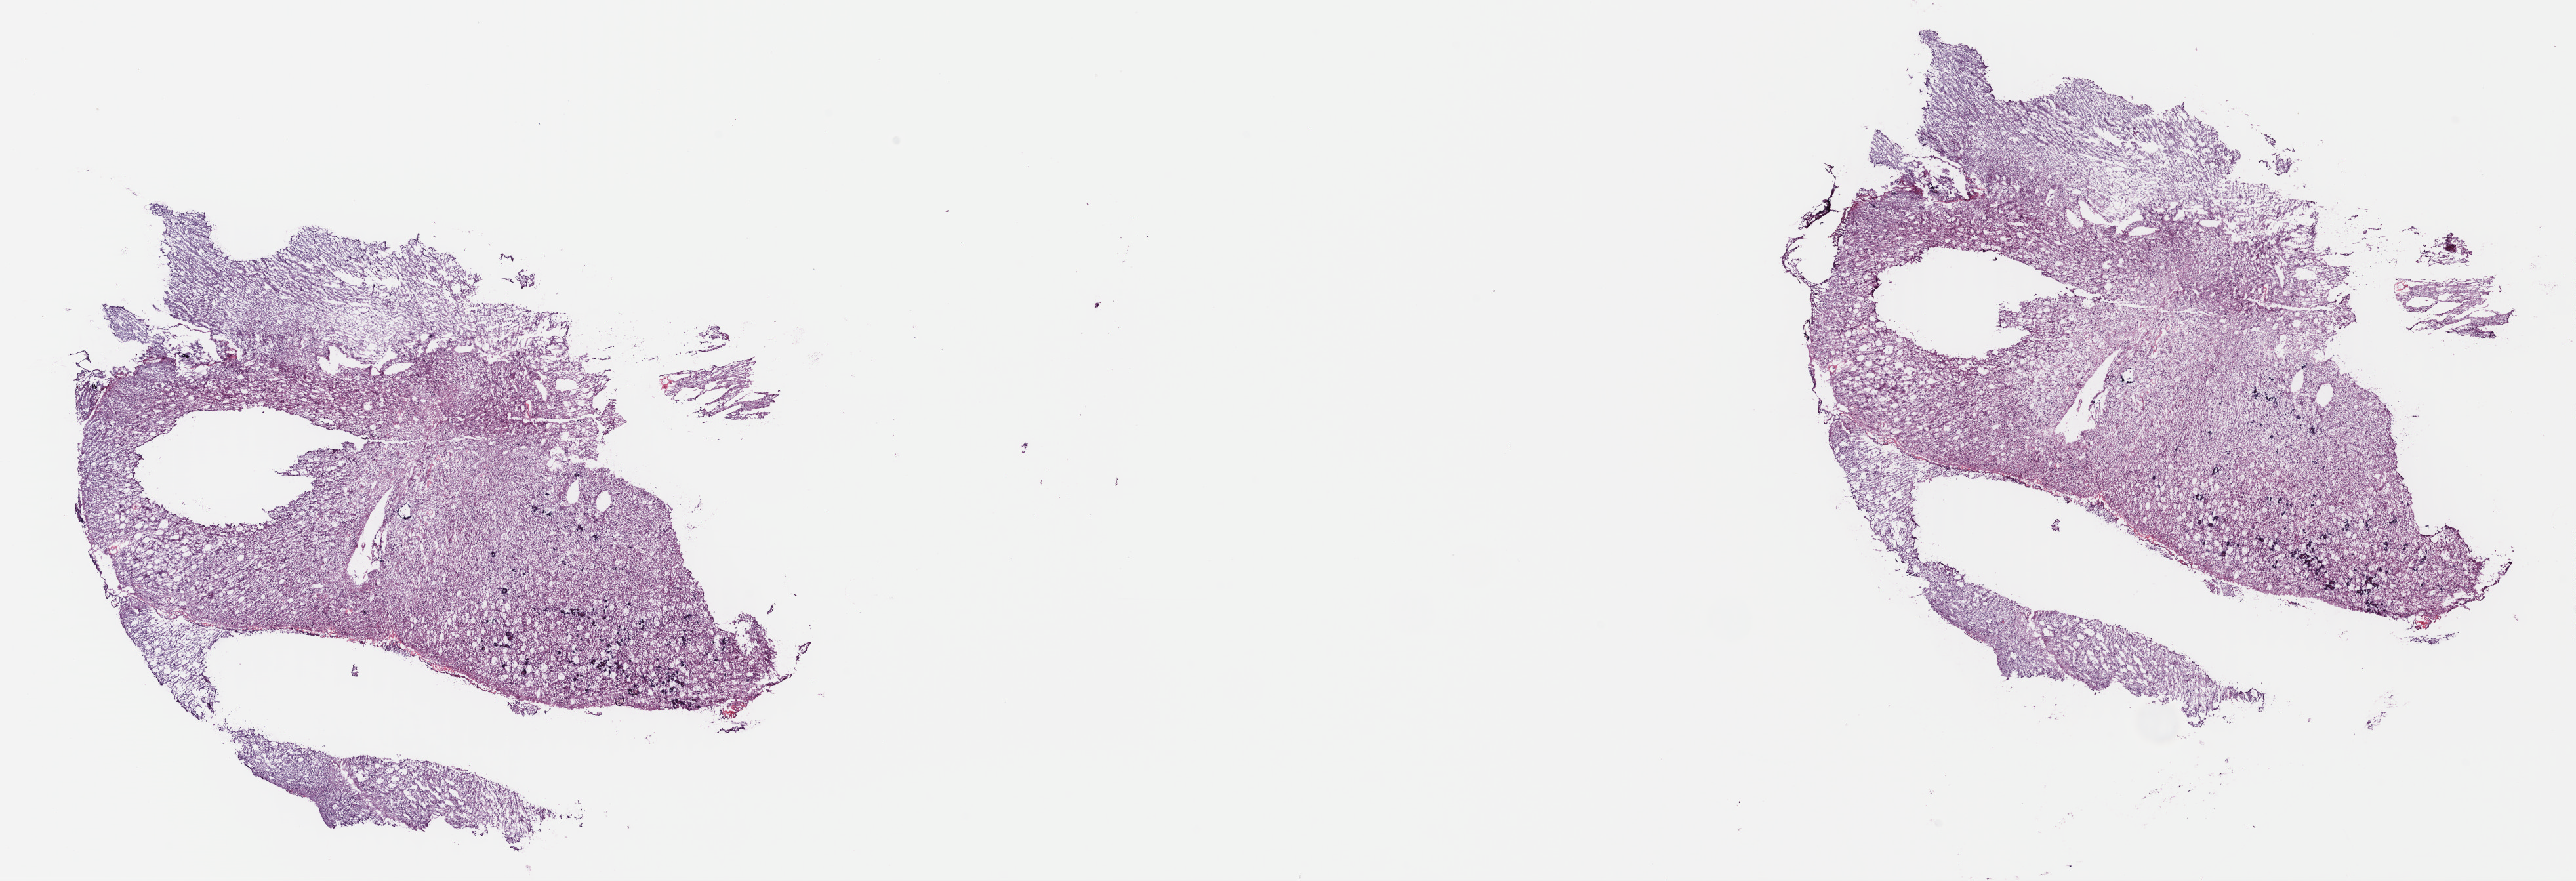
H&E whole-slide image, shown as a low-resolution overview of the whole scanned area (about 30.9 x 10.6 mm), frozen section from the top of the tissue portion, sample: primary tumour, brain. Patient: male, age at initial diagnosis 51 years. Histologic grade: G3 (poorly differentiated). Pathologist review of this section (percent, as recorded): tumour cells 50%, tumour nuclei 70%, normal cells 0%, stromal cells 50%, necrosis 0%. Infiltration values recorded for this section: lymphocyte infiltration 0%, monocyte infiltration 0%, neutrophil infiltration 0%.
Pathologic diagnosis: Oligodendroglioma, anaplastic.